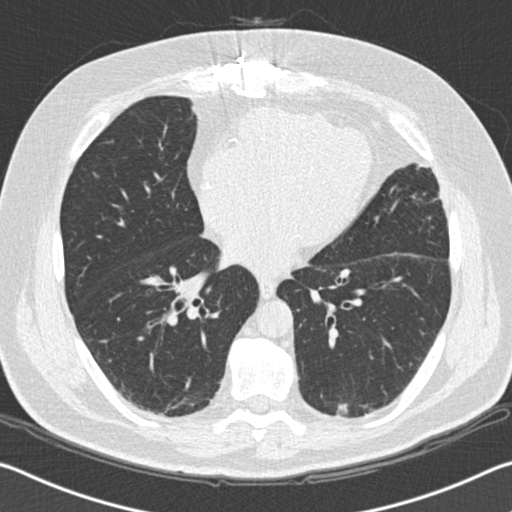
Low-dose screening chest CT, one axial slice. Slice 77 of 172 in the series (ordered by position). Reconstruction kernel B30f. 120 kVp. Lung window (W 1500 / L -600 HU). 2 mm slice thickness. 512 × 512 image matrix.
Structures marked on this image (expert manual segmentation):
- lesion 1 (tumor, lower lobe of left lung): bounding box [x1, y1, x2, y2] px = [337, 403, 370, 416]